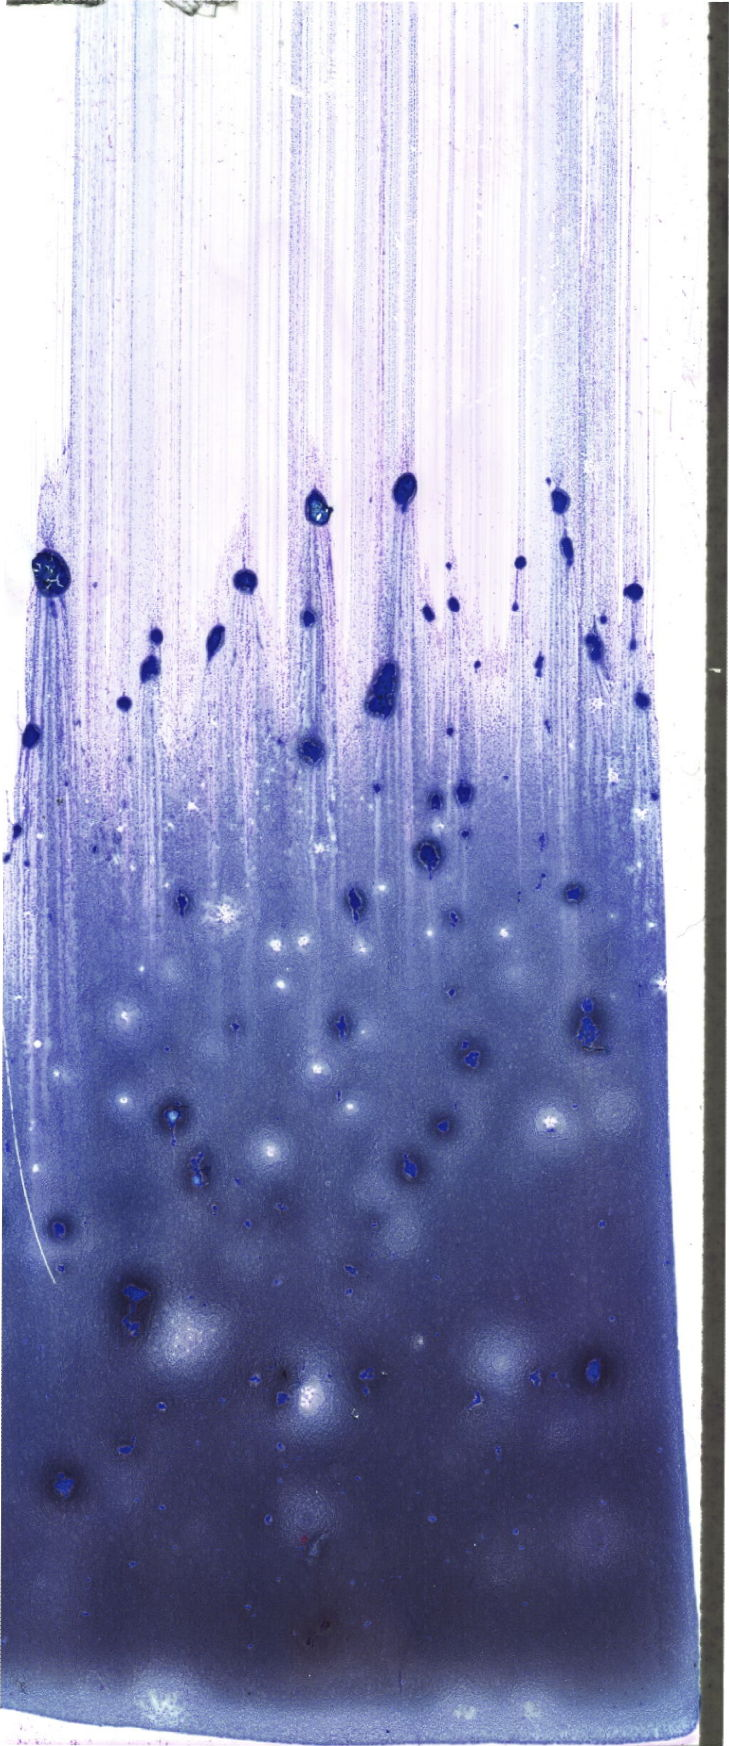
Whole-slide image of a May-Grünwald–Giemsa-stained bone marrow aspirate smear, shown as a low-resolution overview of the whole scanned area (about 20.7 x 49.5 mm). Female patient.
• diagnosis: Acute Myeloid Leukemia without Maturation